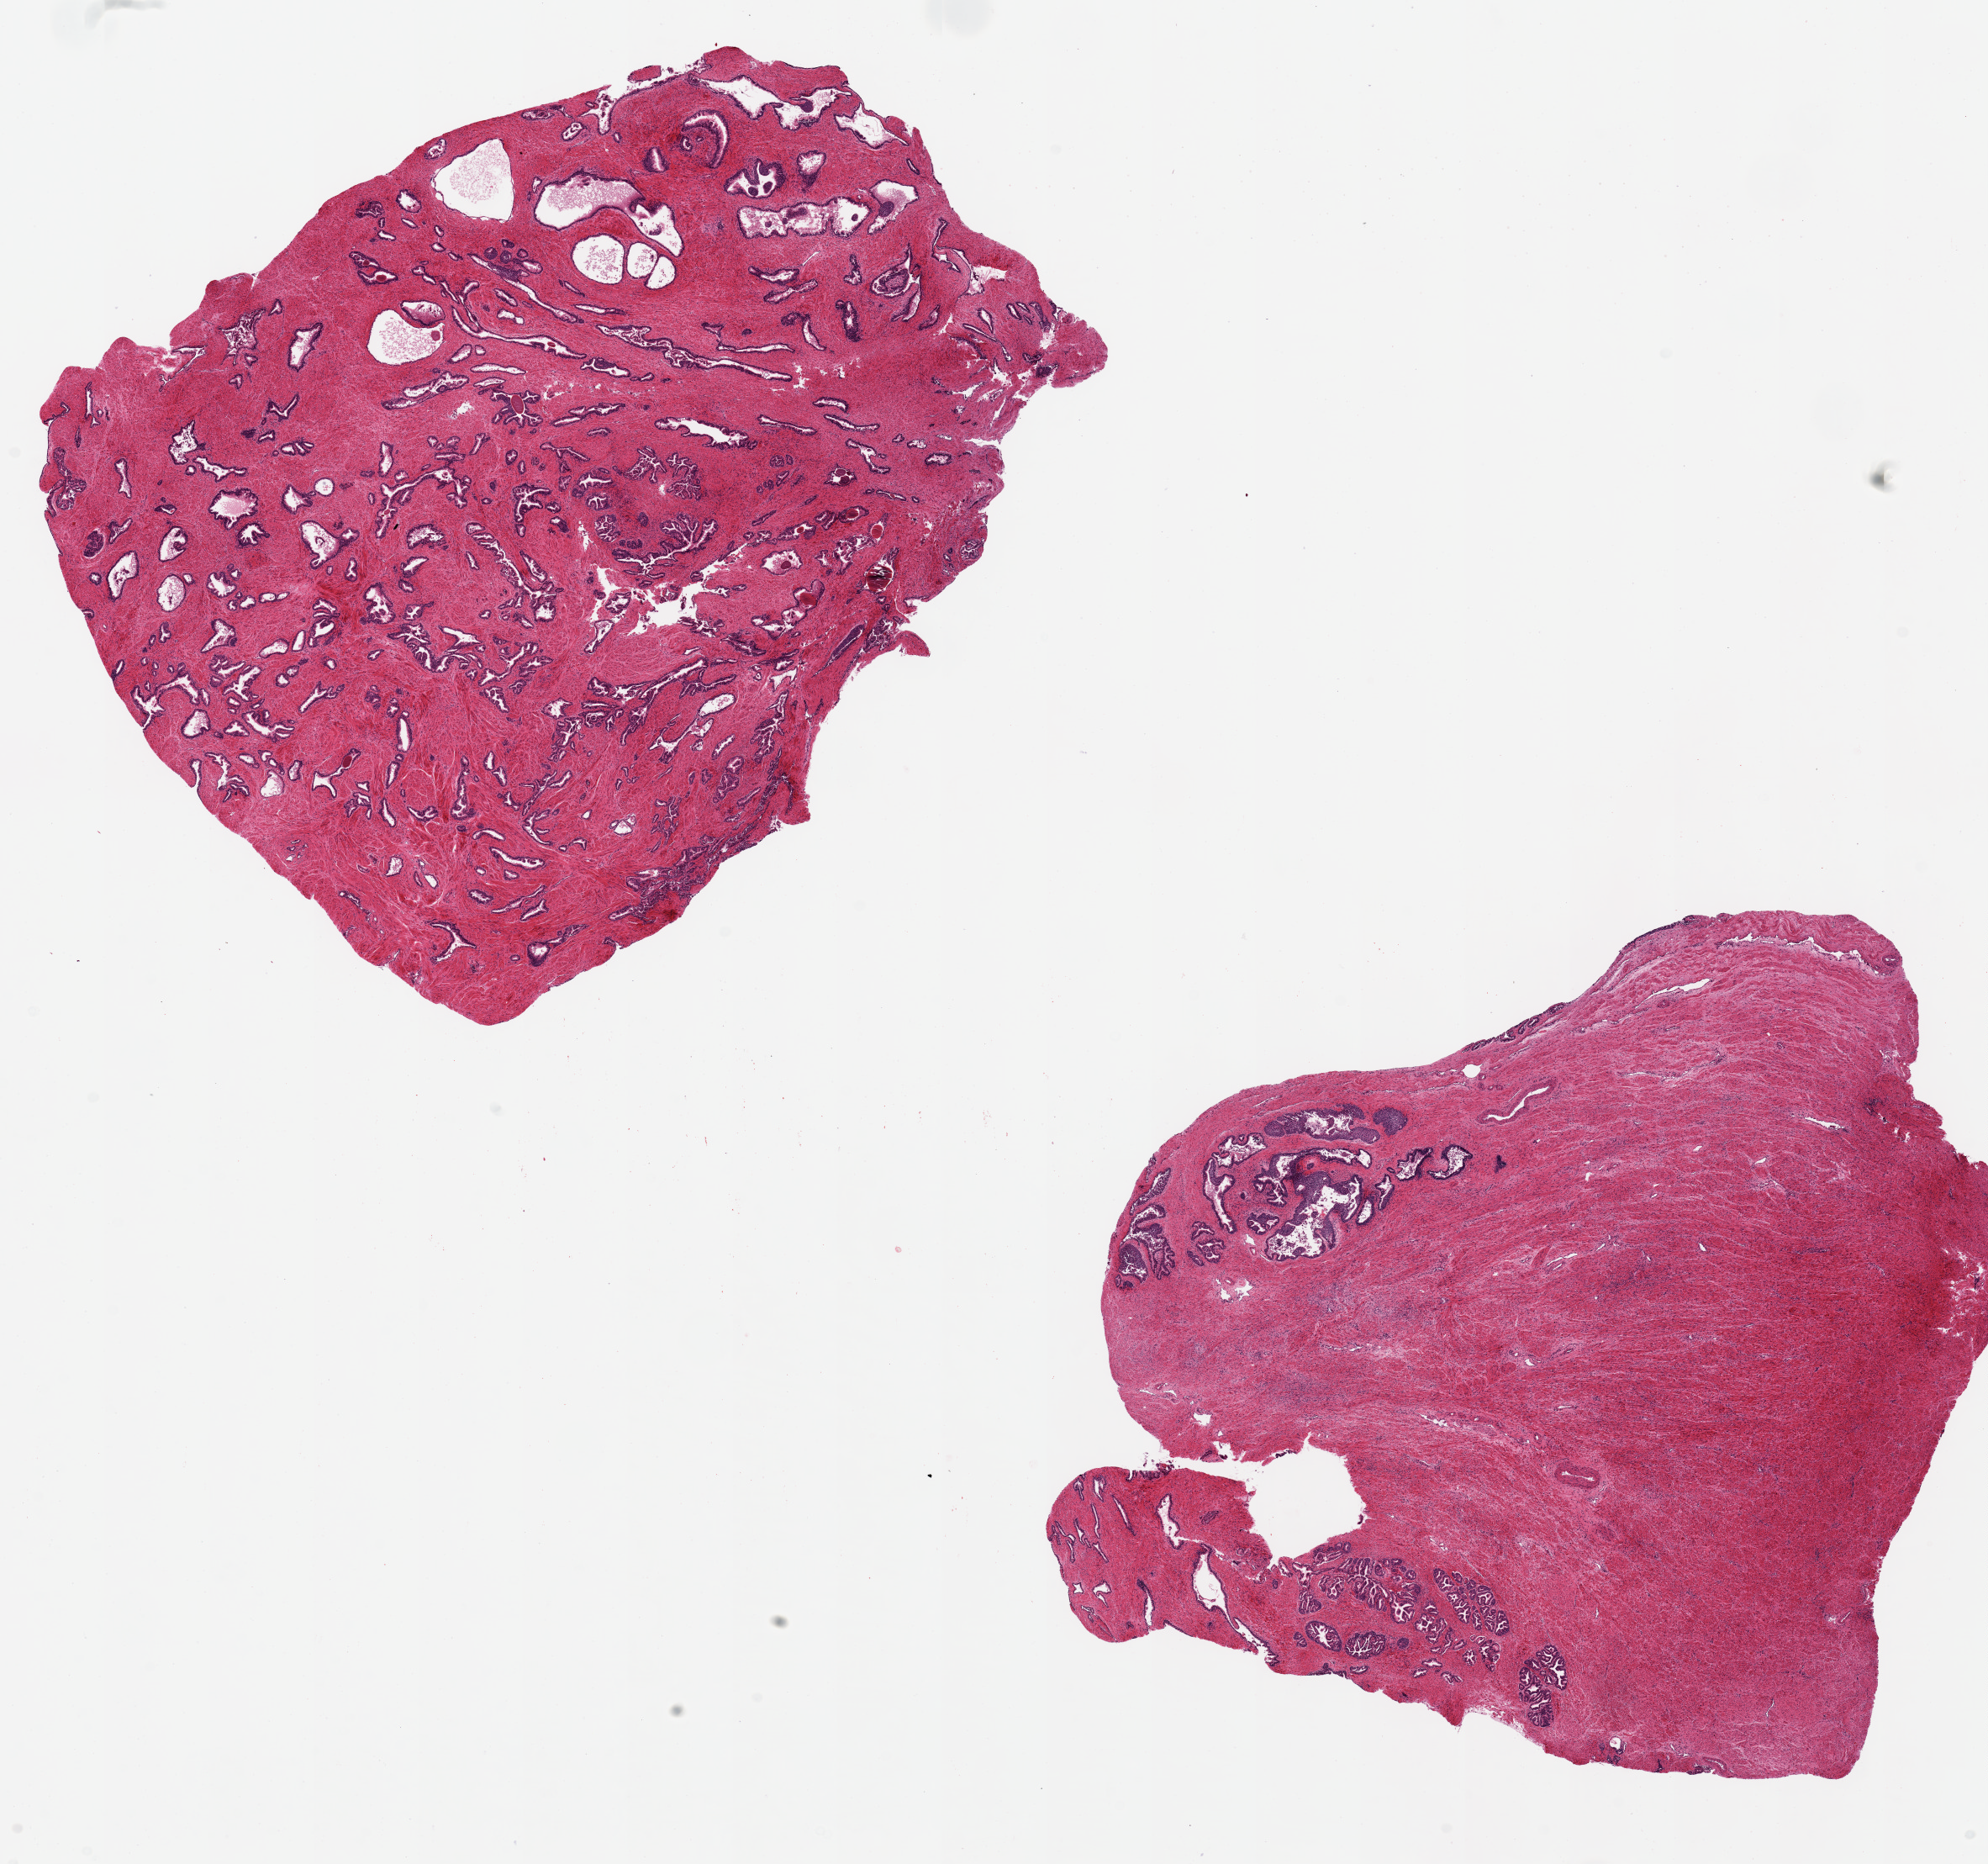
Haematoxylin and eosin whole-slide image — whole scanned area (about 18.7 x 17.5 mm) shown as a low-resolution overview; PAXgene-fixed, paraffin-embedded tissue; target tissue: prostate; donor tissue sample. Male donor.
* review note (as recorded): 2 pieces, 9x7 & 8x8mm; Stromal hyperplasia; 1 has periurethral ducts and glands